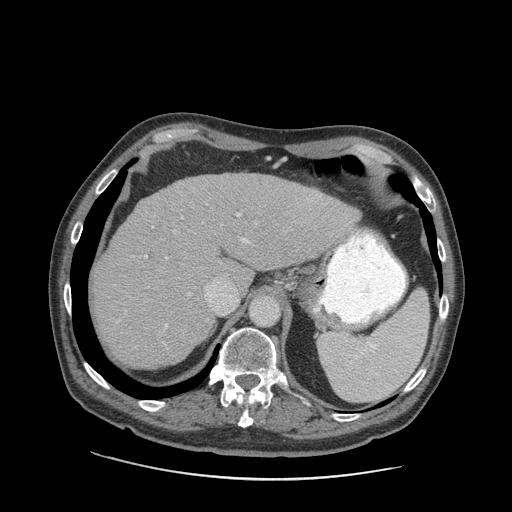
Contrast-enhanced abdominal CT (liver protocol), one axial slice; slice 65 of 89 in the series (ordered by position); reconstruction kernel STANDARD; soft-tissue window (W 400 / L 40 HU); 2.5 mm slice thickness; 512 × 512 image matrix, field of view 420 × 420 mm. Case-level facts recorded for this patient, not image findings: diagnosis: hepatocellular carcinoma (patient treated with transarterial chemoembolisation; whether this scan precedes or follows treatment is not stated here); TNM stage (as recorded): Stage-I; Child-Pugh class: A; tumour differentiation: moderately differentiated; tumour nodularity: uninodular.
Structures marked on this image (semi-automatically segmented with operator editing):
- liver parenchyma outside the tumour (the mass and vessels are separate outlines, so this box may not span the whole liver): bounding box [x1, y1, x2, y2] px = [94, 172, 358, 368]
- liver vessels: [114, 191, 347, 348]